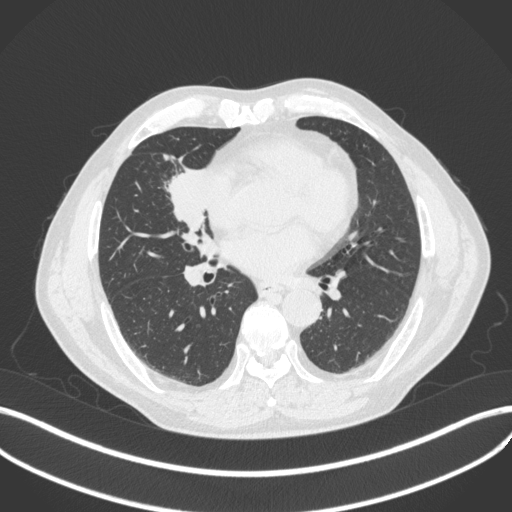
Chest CT, one axial slice. Position 185 of 429 along the scan axis. 120 kVp. Lung window (W 1500 / L -600 HU). 512 × 512 image matrix, field of view 400 × 400 mm. Patient: male, 61 years. From the clinical record (not read from this slice): clinical TNM (as recorded): T2b N1 M0.
Annotated regions visible in this slice (rectangle marked by the reading radiologist):
- lung tumour (recorded histology: squamous cell carcinoma): bounding box [x1, y1, x2, y2] px = [159, 160, 215, 232]